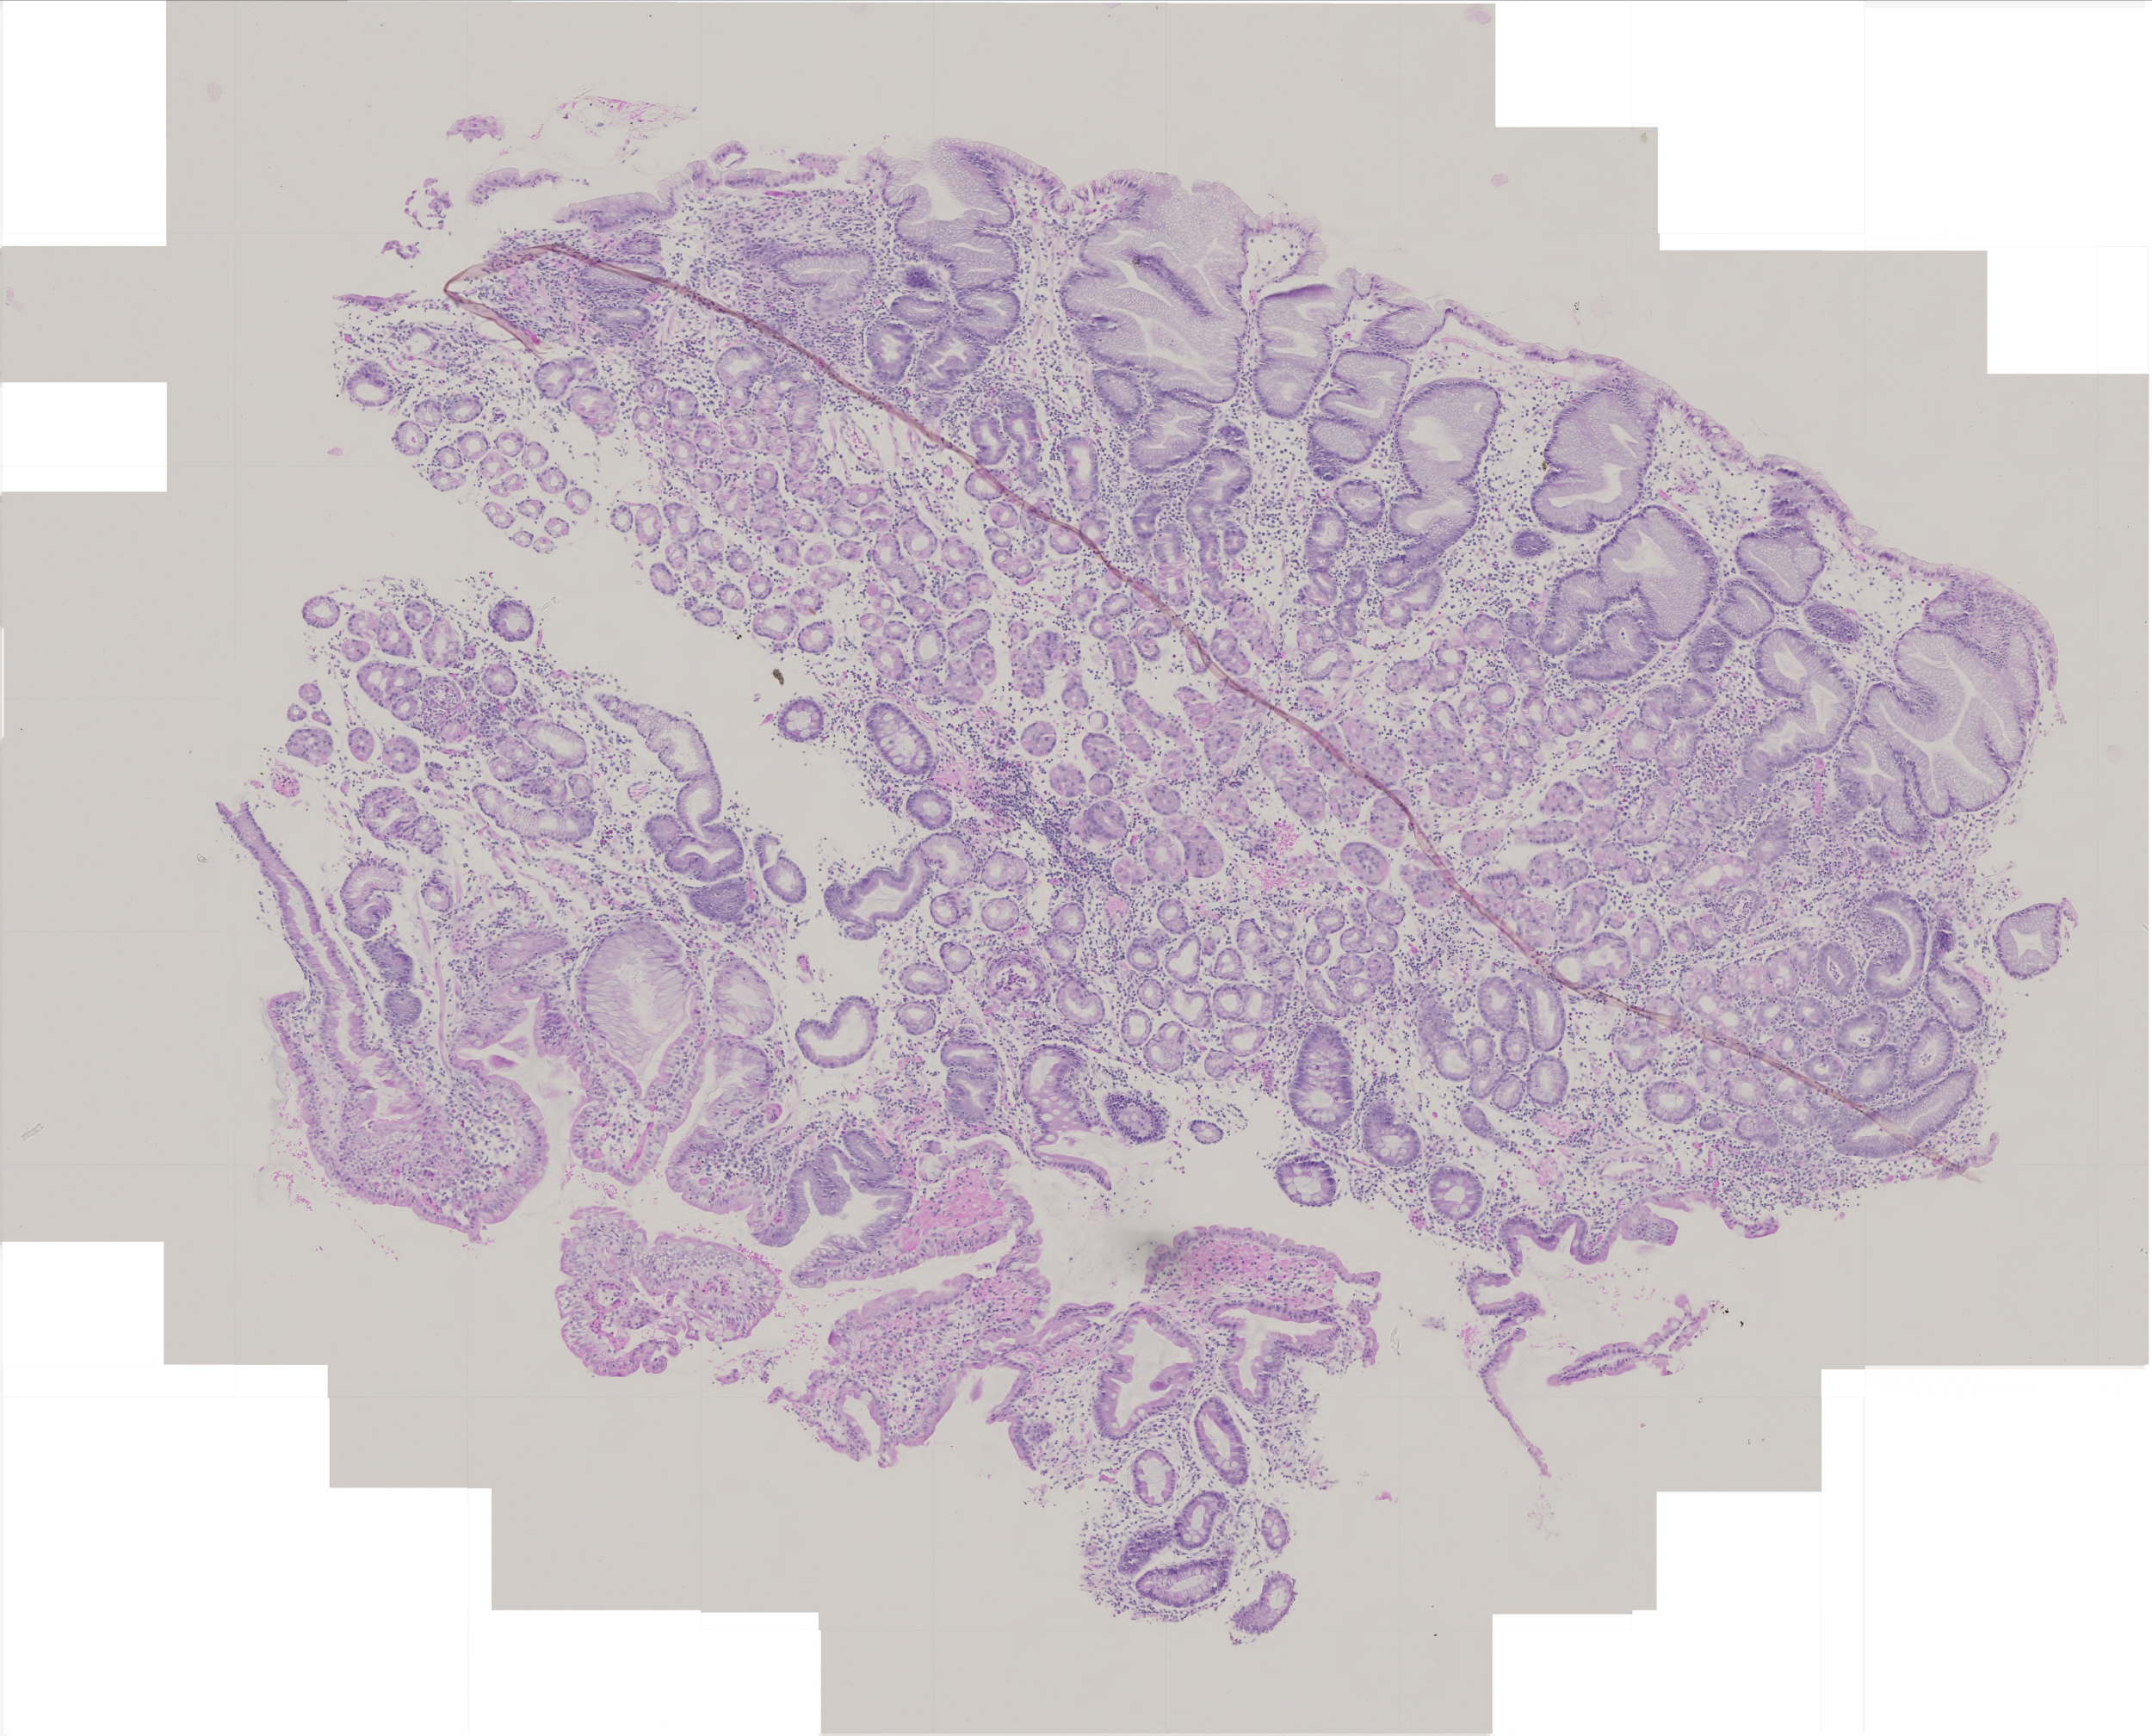
H&E-stained whole-slide image, low-resolution overview of the scanned area, about 5.0 x 4.0 mm. FFPE section. Stomach, primary tumour sample. Patient: female, age at initial diagnosis 67 years. Histologic grade: G3 (poorly differentiated).
Pathologic diagnosis: Adenocarcinoma, intestinal type (body of stomach). Lymph nodes positive (case pathology): 15 of 21 examined. AJCC pathologic stage: IV (5th edition).